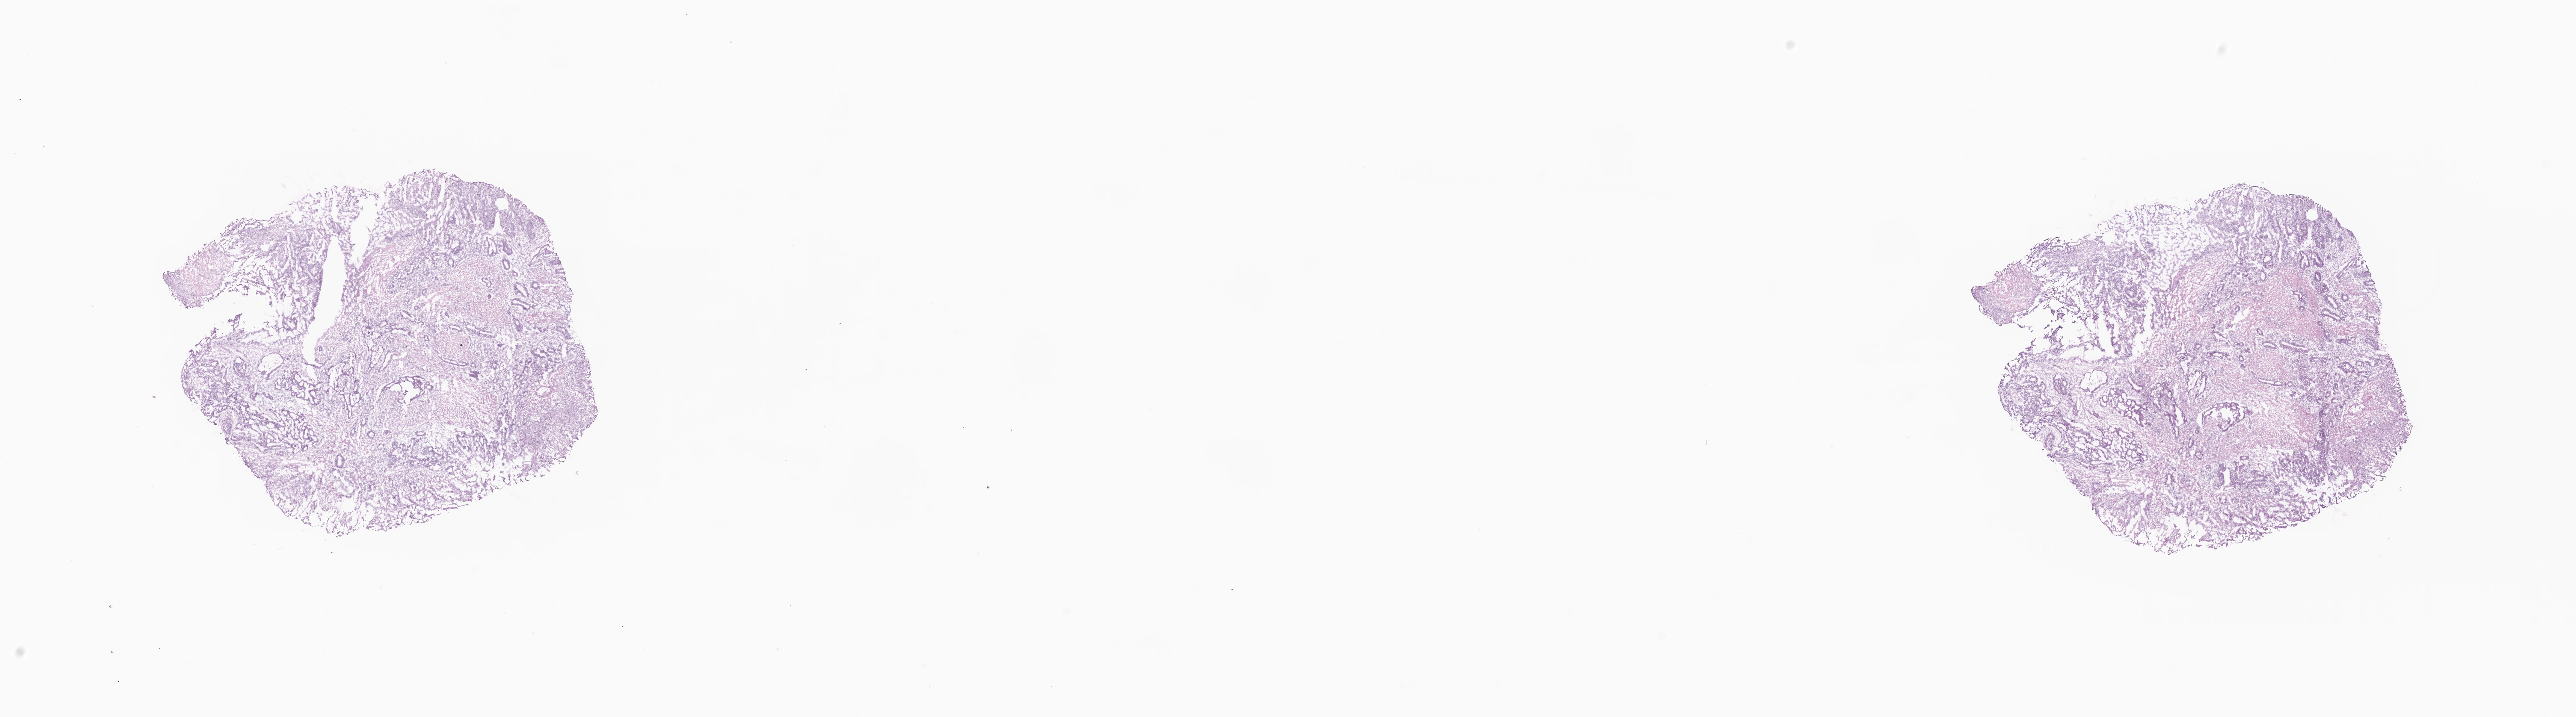
Digitized haematoxylin and eosin-stained section, low-resolution overview of the scanned area, about 28.9 x 8.0 mm; cryosection; primary tumor; site: rectosigmoid junction. Male, age 63 years at initial diagnosis. Pathologist review of this section (percent, as recorded): tumor cells 37%, tumor nuclei 36%, stromal cells 60%, necrosis 3%, normal cells 0%. Inflammatory infiltration, as recorded: lymphocyte infiltration 58%, monocyte infiltration 2%, neutrophil infiltration 0%.
* diagnosis: Adenocarcinoma, NOS
* section: top of the tissue portion